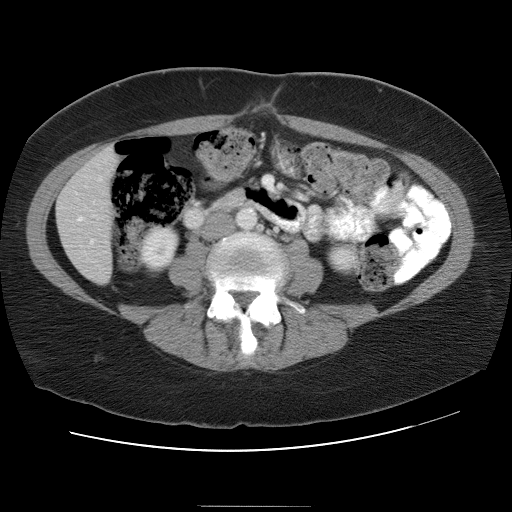
Contrast-enhanced abdominal CT, one axial slice. Slice 7 of 30 in the series (ordered by position). Reconstruction kernel STANDARD. 120 kVp. Intravenous contrast given. Soft-tissue window (W 400 / L 40 HU). 7.5 mm slice thickness. 512 × 512 image matrix, field of view 376 × 376 mm. Female patient, age 52 years. From the clinical record (not read from this slice): diagnosis: colorectal cancer liver metastases, imaged before liver resection; multiple liver metastases: no; largest metastasis: 3 cm; chemotherapy before resection: yes.
Outlined on this slice (manually delineated by an expert):
- hepatic veins: bounding box <78,218,82,221> (left, top, right, bottom; pixels)
- liver: <57,148,118,283>
- portal vein (with intrahepatic branches): <90,240,94,243>